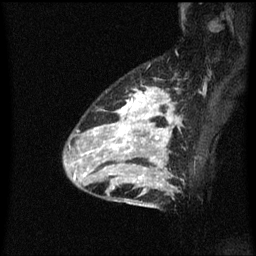
Breast MRI (dynamic contrast-enhanced), one sagittal slice; position 44 of 60 along the scan axis; dynamic contrast-enhanced series, image 2 of 3 at this slice position (ordered by acquisition); 1.5 T; TE 4.2 ms, TR 8.4 ms; 2 mm slice thickness; 256 × 256 image matrix. Female patient, age 34 years. Case-level facts recorded for this patient, not image findings: setting: breast cancer imaged before/during neoadjuvant chemotherapy; receptor status: HR-positive, HER2-negative.
Annotated regions visible in this slice (semi-automatically segmented with operator editing):
- analysis volume of interest (the breast-tissue region the enhancement analysis was run in; not a lesion): bounding box [x1, y1, x2, y2] px = [69, 88, 180, 209]
- tumour enhancement mask (voxels above the 70 % enhancement threshold inside the analysis volume of interest): [74, 88, 175, 179]